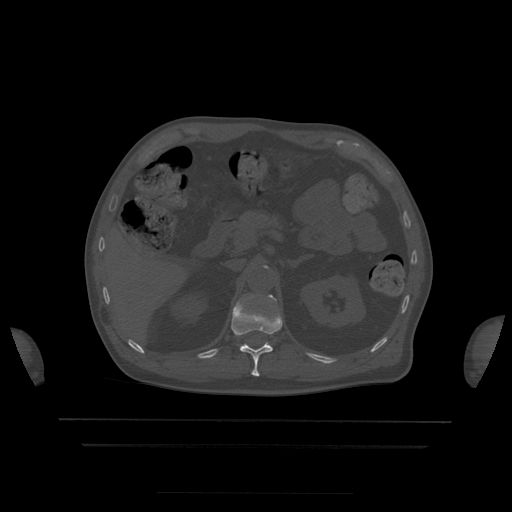
CT including the spine, one axial slice; position 190 of 522 along the scan axis; bone window (W 1800 / L 400 HU); 1.25 mm slice thickness; 512 × 512 image matrix, field of view 436 × 436 mm. Patient age 68 years. From the clinical record (not read from this slice): primary cancer: urothelial.
Annotated regions visible in this slice (semi-automatically segmented with operator editing):
- L1 vertebra: bounding box <260,295,277,305> (left, top, right, bottom; pixels)
- T12 vertebra: <232,302,283,377>